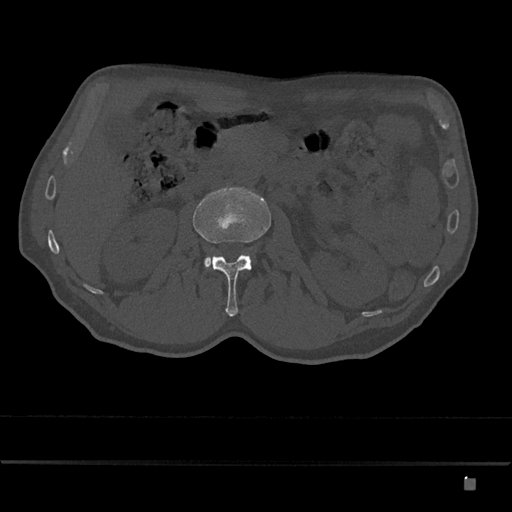
CT including the spine, one axial slice. Position 462 of 797 along the scan axis. 120 kVp. Bone window (W 1800 / L 400 HU). 512 × 512 image matrix, field of view 390 × 390 mm. Male patient, age 72 years. From the clinical record (not read from this slice): primary cancer: prostate.
Outlined on this slice (semi-automatically segmented with operator editing):
- L2 vertebra: bounding box <192,186,271,317> (left, top, right, bottom; pixels)
- L3 vertebra: <204,257,213,268>